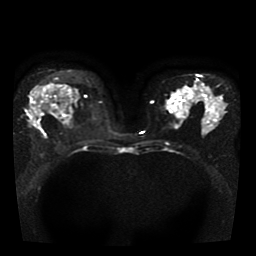
Breast MRI, one axial slice; position 24 of 41 along the scan axis; diffusion-weighted series; image 2 of 4 stored at this slice position (different b-values; order by instance number); 1.5 T; 5 mm slice thickness; 256 × 256 image matrix. Female patient.
Annotated regions visible in this slice (outlined manually by an expert reader):
- tumour on diffusion-weighted imaging: bounding box [x1, y1, x2, y2] px = [31, 90, 43, 129]